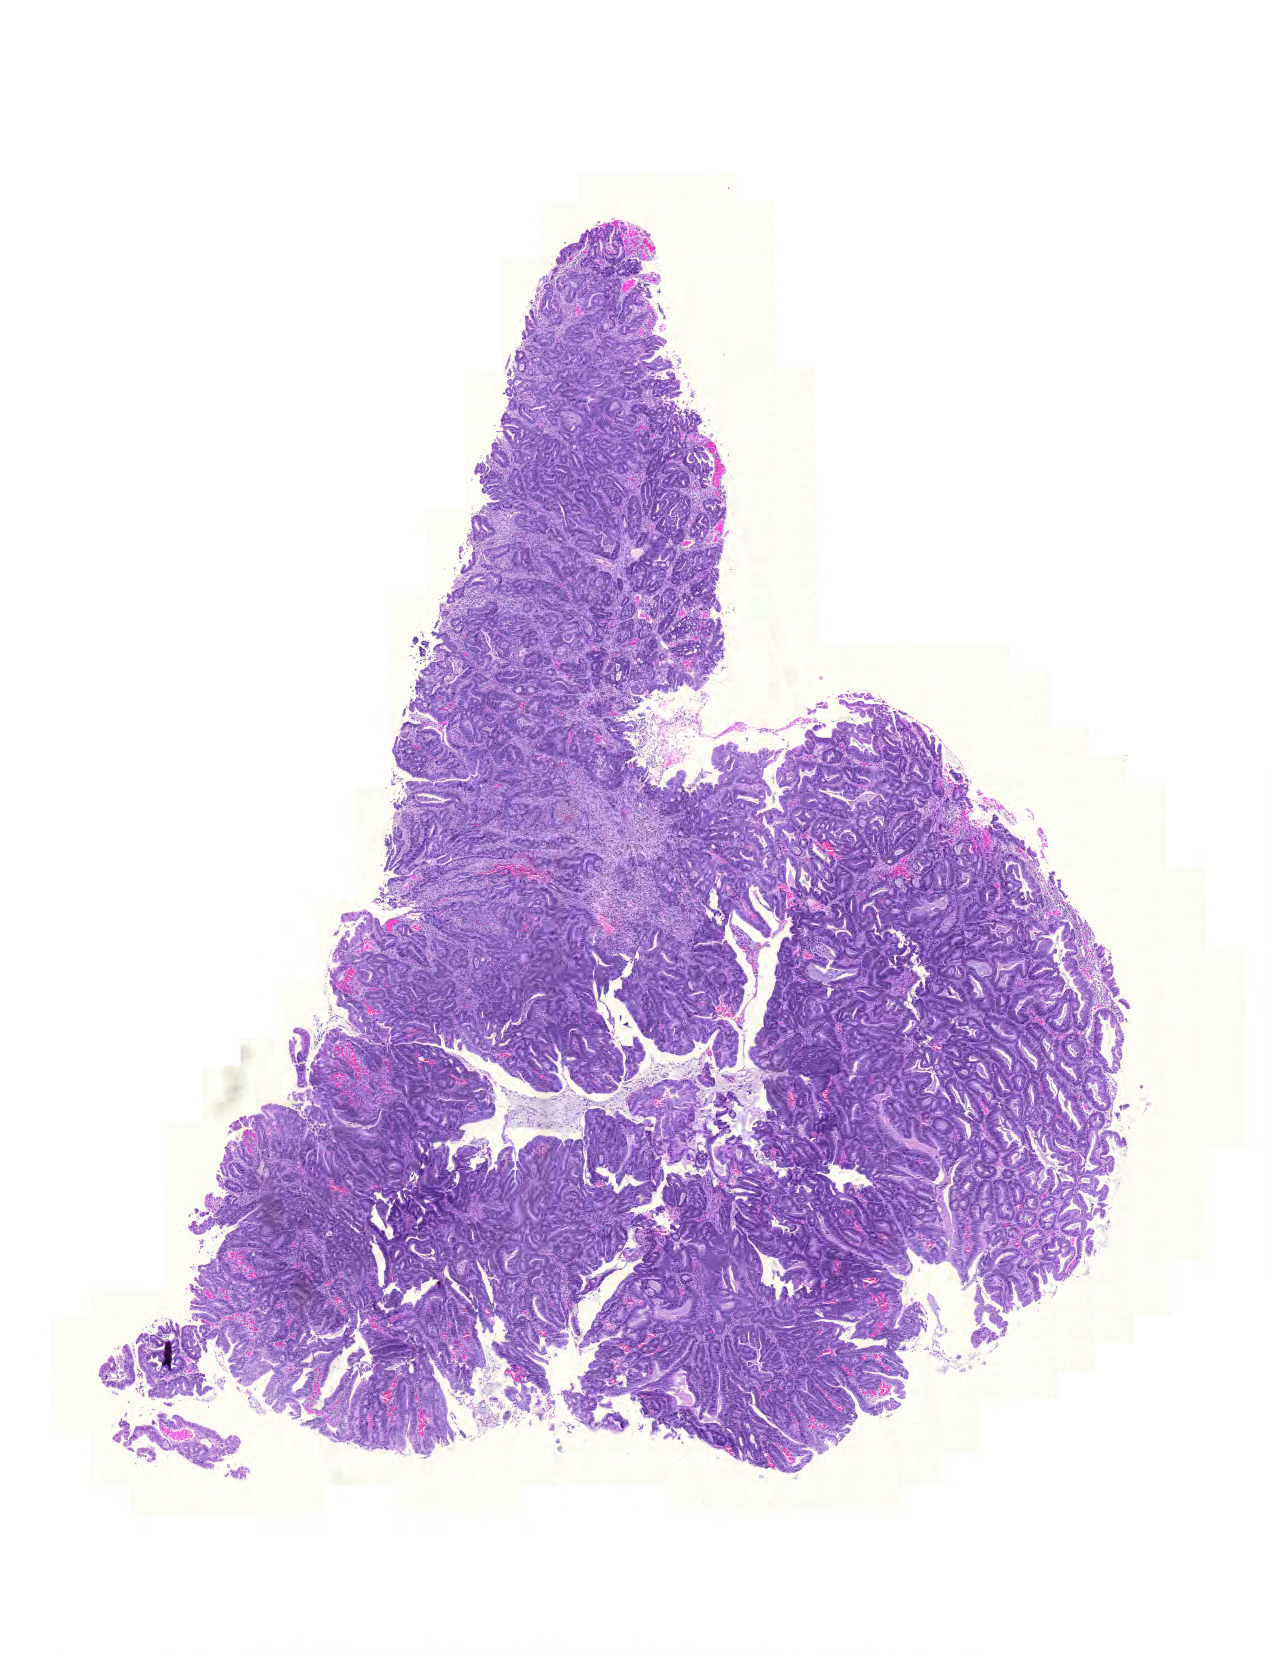
Hematoxylin and eosin (H&E) stained whole-slide image — a low-resolution overview of the entire scanned area, about 9.5 x 12.3 mm (from a 20x scan); formalin-fixed paraffin-embedded (FFPE) diagnostic section; sample: primary tumour, colon. Male patient; age at initial diagnosis 84 years.
* AJCC pathologic stage: I
* lymph nodes positive (case pathology): 0 of 25 examined
* histologic diagnosis: Mucinous adenocarcinoma (ascending colon)